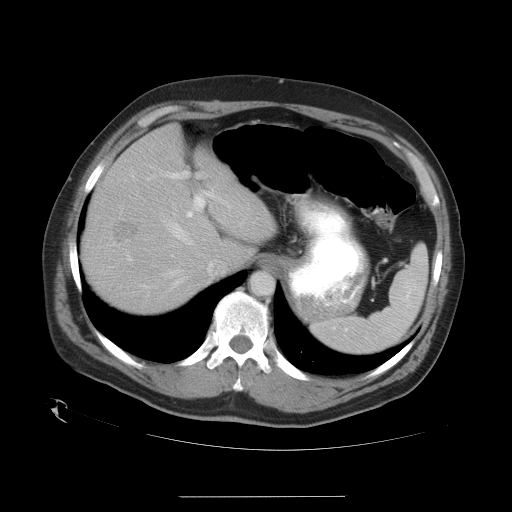
Contrast-enhanced abdominal CT, one axial slice; slice 25 of 35 in the series (ordered by position); reconstruction kernel STANDARD; 120 kVp; intravenous contrast given; soft-tissue window (W 400 / L 40 HU); 7.5 mm slice thickness; 512 × 512 image matrix. Male patient, age 67 years. From the clinical record (not read from this slice): diagnosis: colorectal cancer liver metastases, imaged before liver resection; multiple liver metastases: no; largest metastasis: 2.3 cm; disease in both lobes: no.
Outlined on this slice (manually delineated by an expert):
- hepatic veins: bounding box <125,166,195,291> (left, top, right, bottom; pixels)
- liver: <84,127,273,315>
- planned liver remnant (the part of the liver to remain after resection): <92,127,273,315>
- portal vein (with intrahepatic branches): <128,171,232,260>
- liver metastasis: <114,223,140,242>